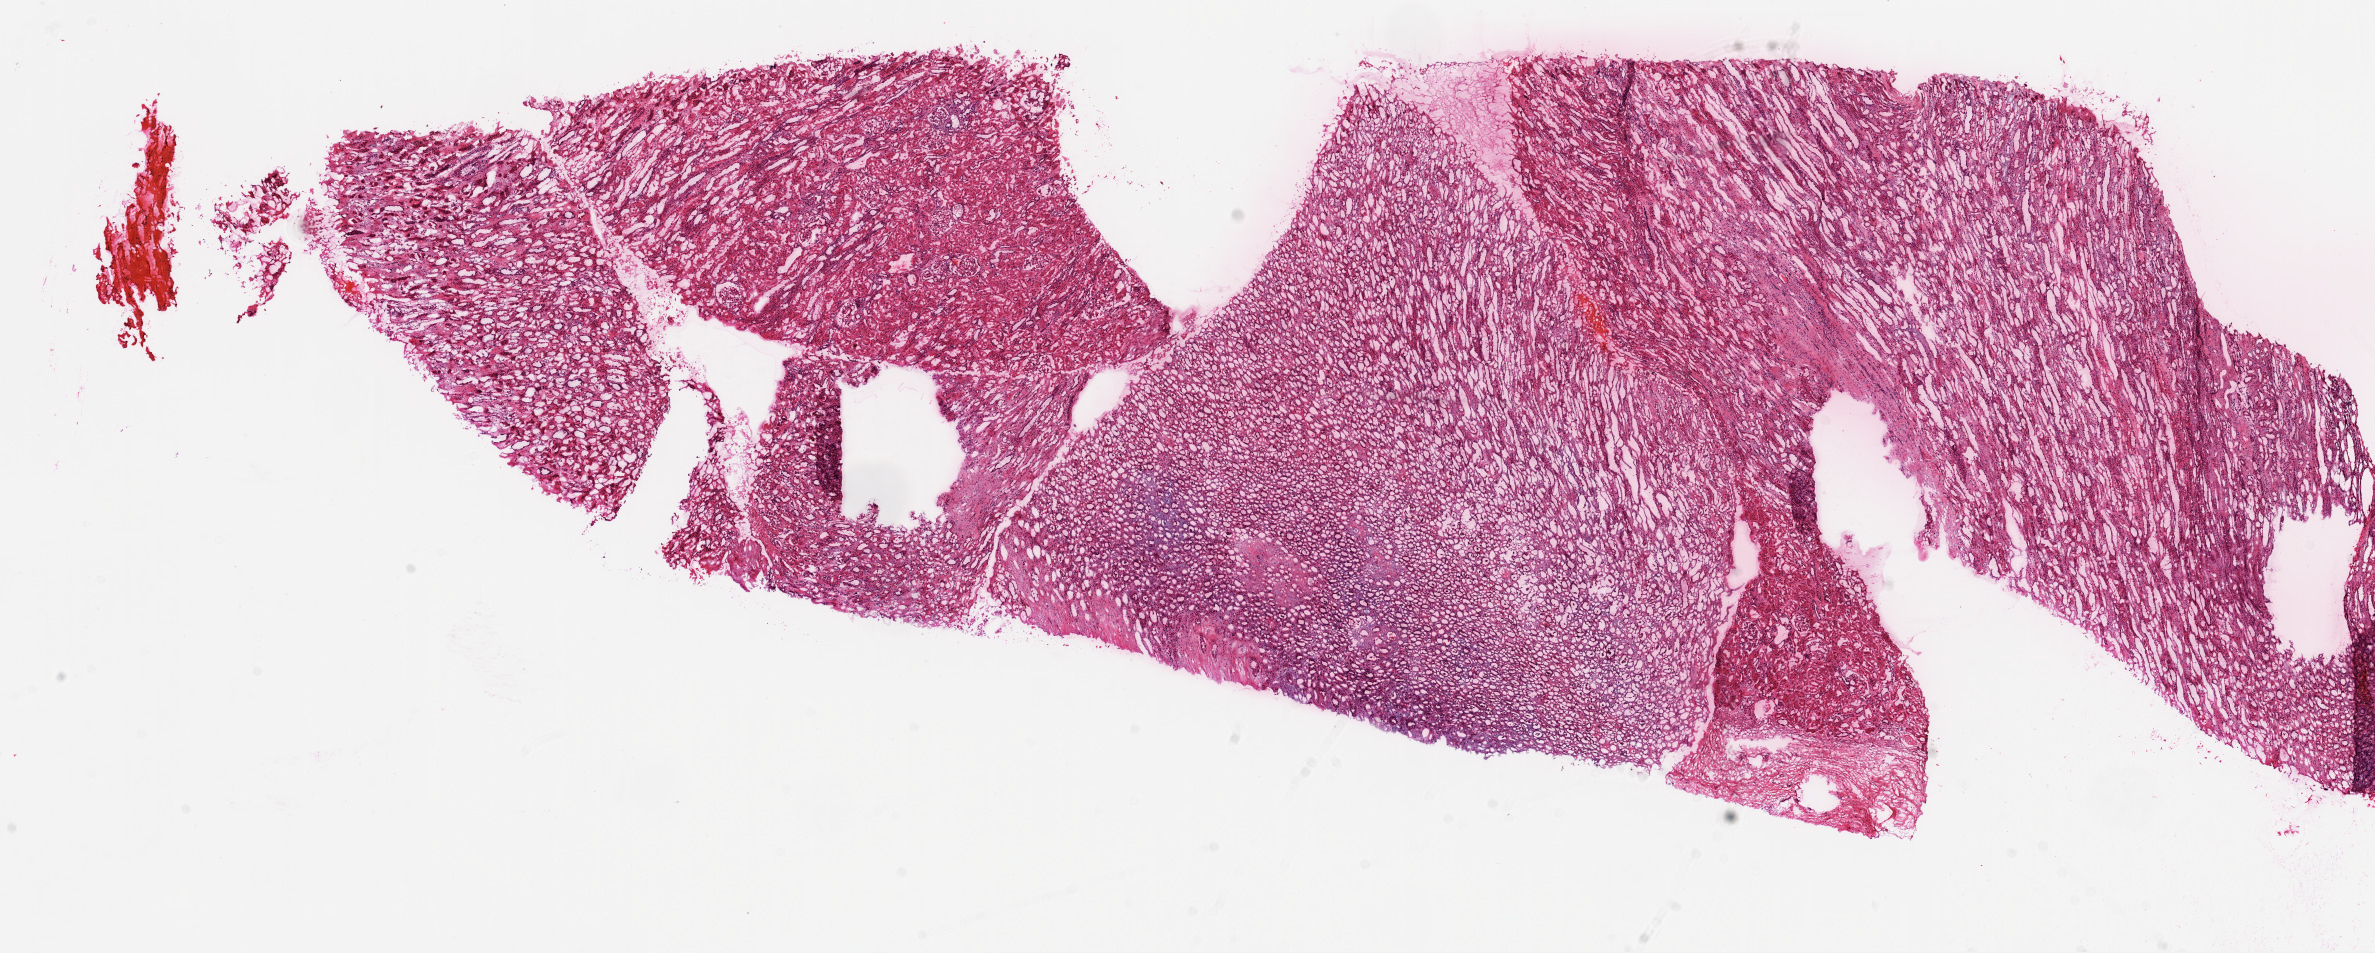
Whole-slide histology image, H&E-stained — a low-resolution overview of the entire scanned area, about 19.1 x 7.6 mm (from a 20x scan); frozen section from the top of the tissue portion; sample: solid tissue normal (non-tumour tissue), kidney. Male, age 61 years at initial diagnosis.
This section: solid tissue normal (non-tumour) sample from the same patient. Patient diagnosis: Clear cell adenocarcinoma, NOS.